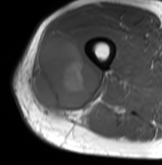
MRI of an extremity soft-tissue mass, one axial slice. Slice 37 of 61 in the series (ordered by position). MR volume resampled by the dataset authors to the PET/CT grid (not the native acquisition matrix). 3.27 mm slice thickness. 162 × 165 image matrix, field of view 158 × 161 mm. Male patient. Case-level facts recorded for this patient, not image findings: histological type: poorly differentiated synovial sarcoma; grade: high; site of the primary tumour: right buttock.
Annotated regions visible in this slice (expert contour drawn on MRI and transferred to this co-registered scan by the dataset authors):
- gross tumour volume including surrounding oedema: bounding box [x1, y1, x2, y2] px = [34, 35, 97, 117]
- gross tumour volume (mass): [34, 36, 97, 117]